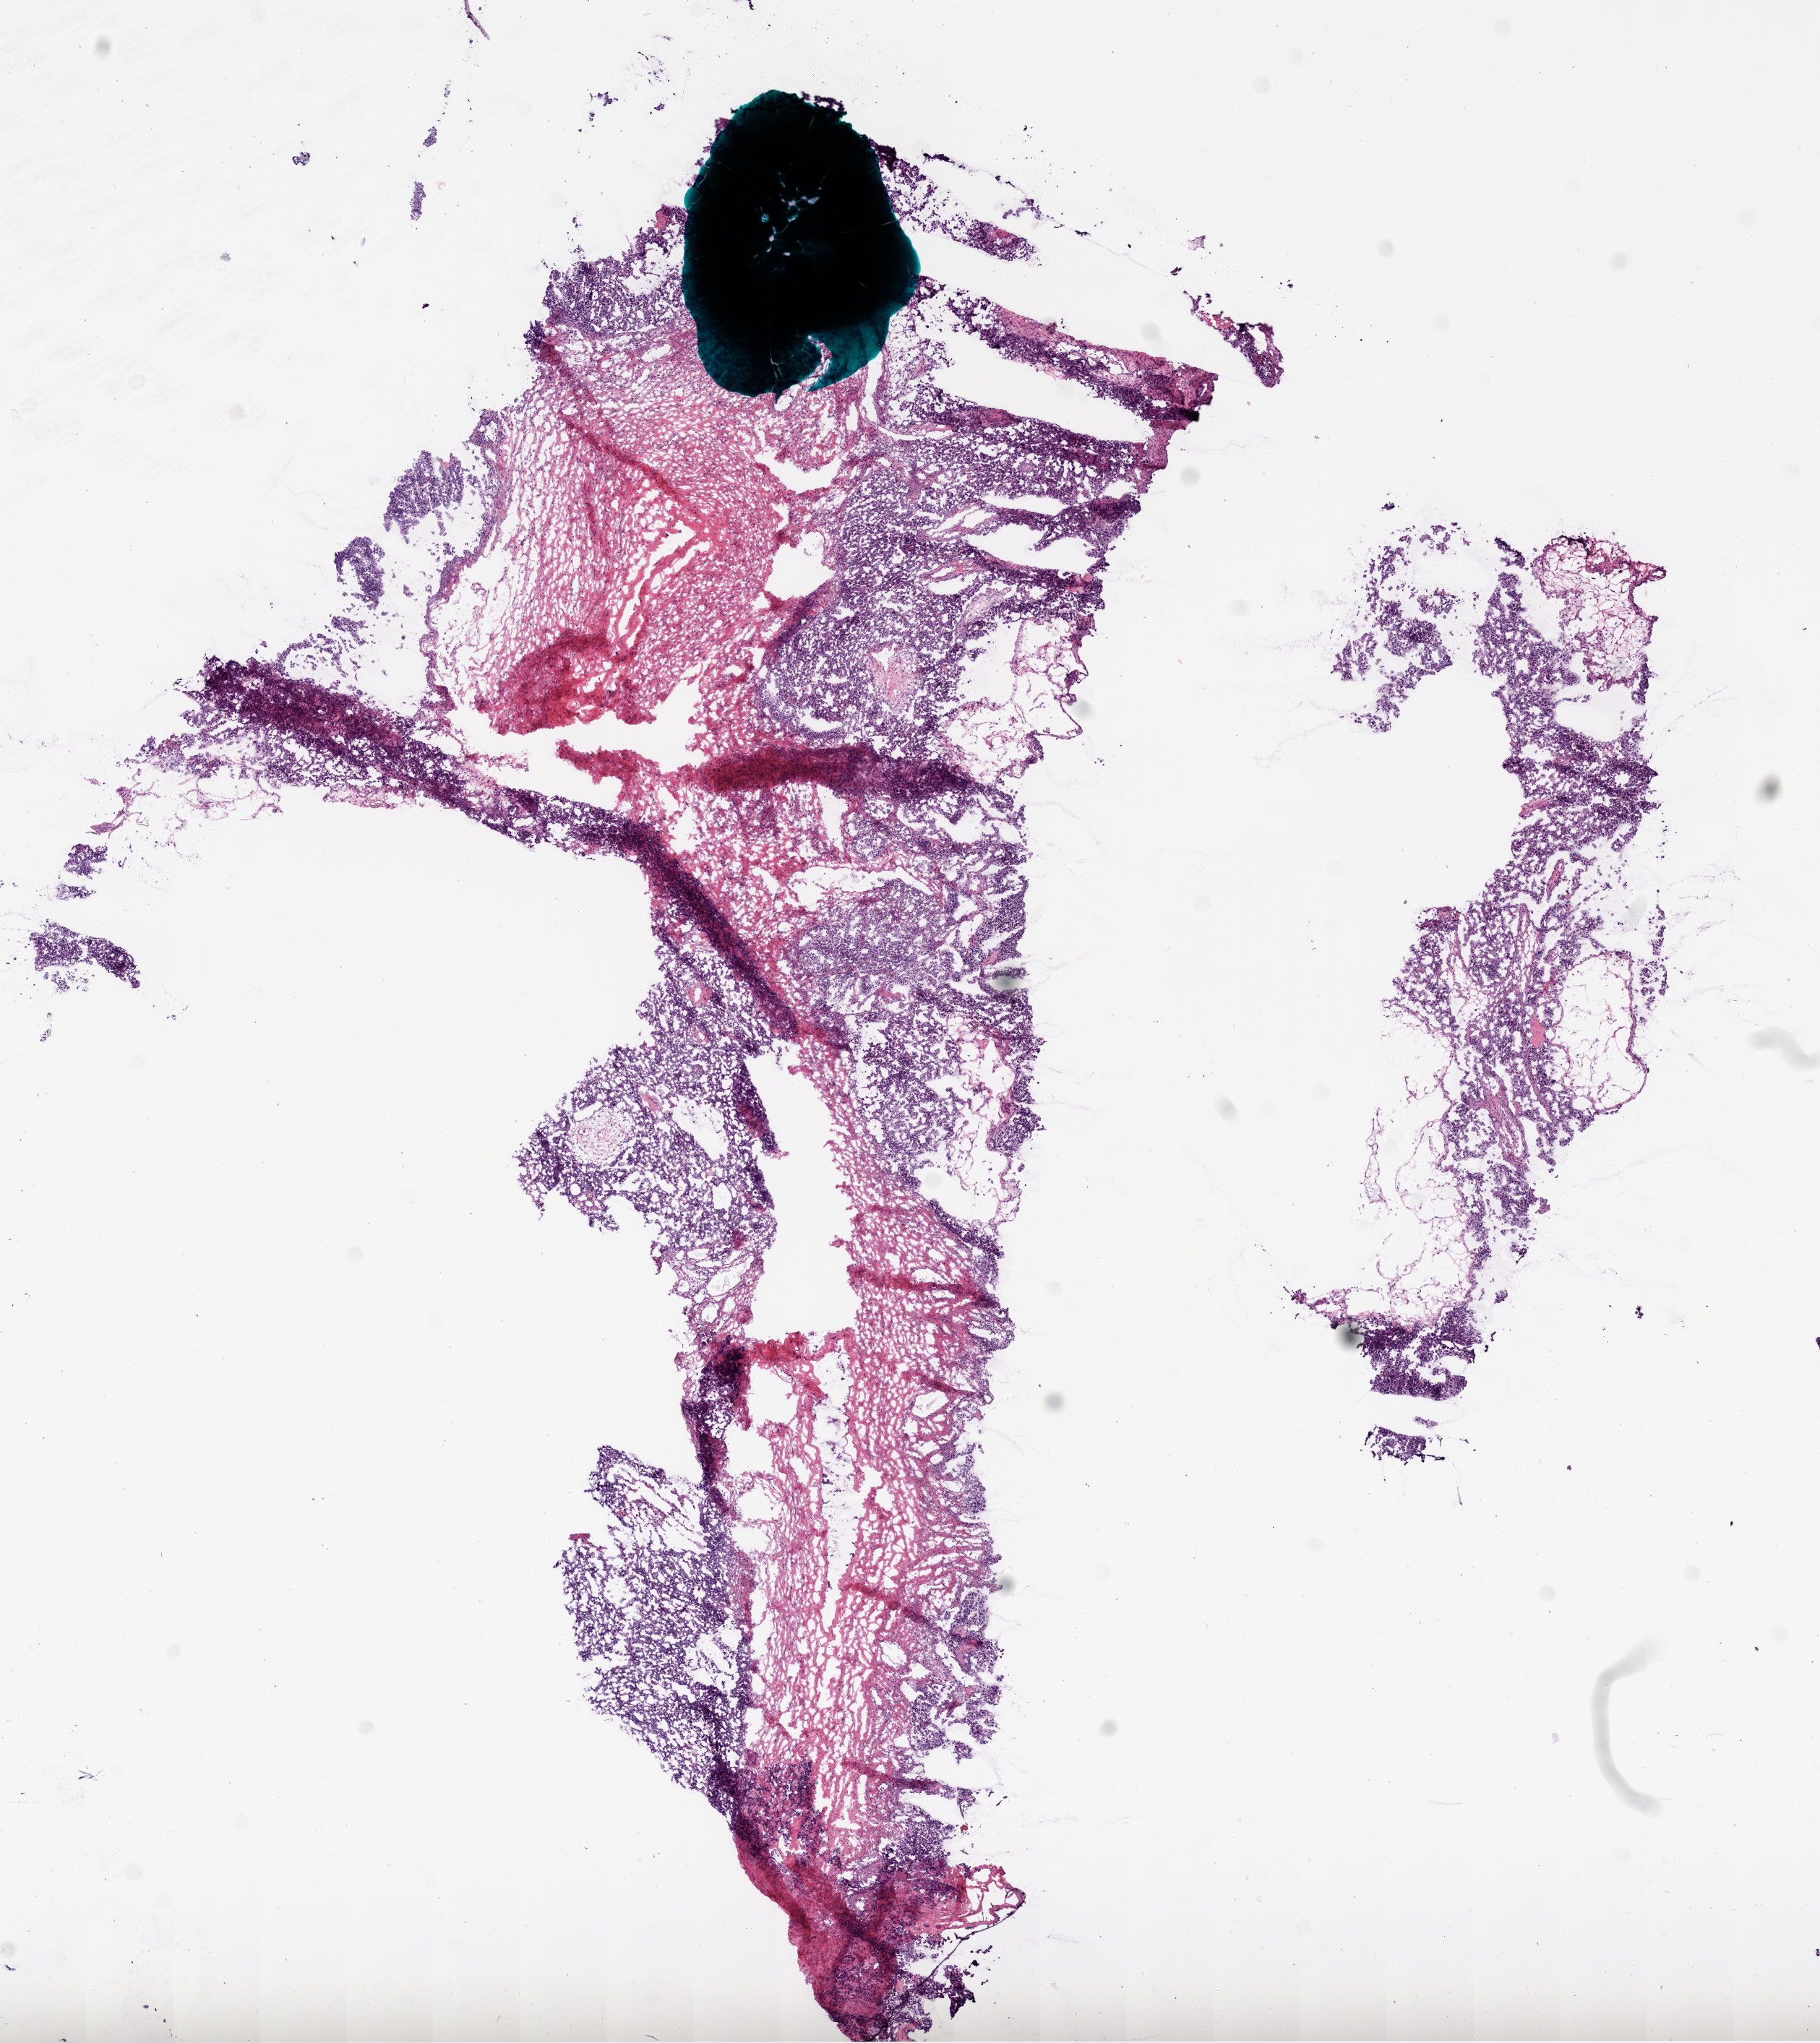
Whole-slide histology image, Hematoxylin and eosin (H&E) stained — low-resolution overview of the scanned area, about 10.2 x 11.4 mm. Frozen section from the bottom of the tissue portion. Sample: primary tumour, ovary. Female, age 65 years at initial diagnosis. Histologic grade: G3 (poorly differentiated). Composition of this section per pathologist review: tumour cells 59%, tumour nuclei 70%, normal cells 0%, stromal cells 40%, necrosis 1%.
Pathologic diagnosis: Serous cystadenocarcinoma, NOS. FIGO stage: IA.